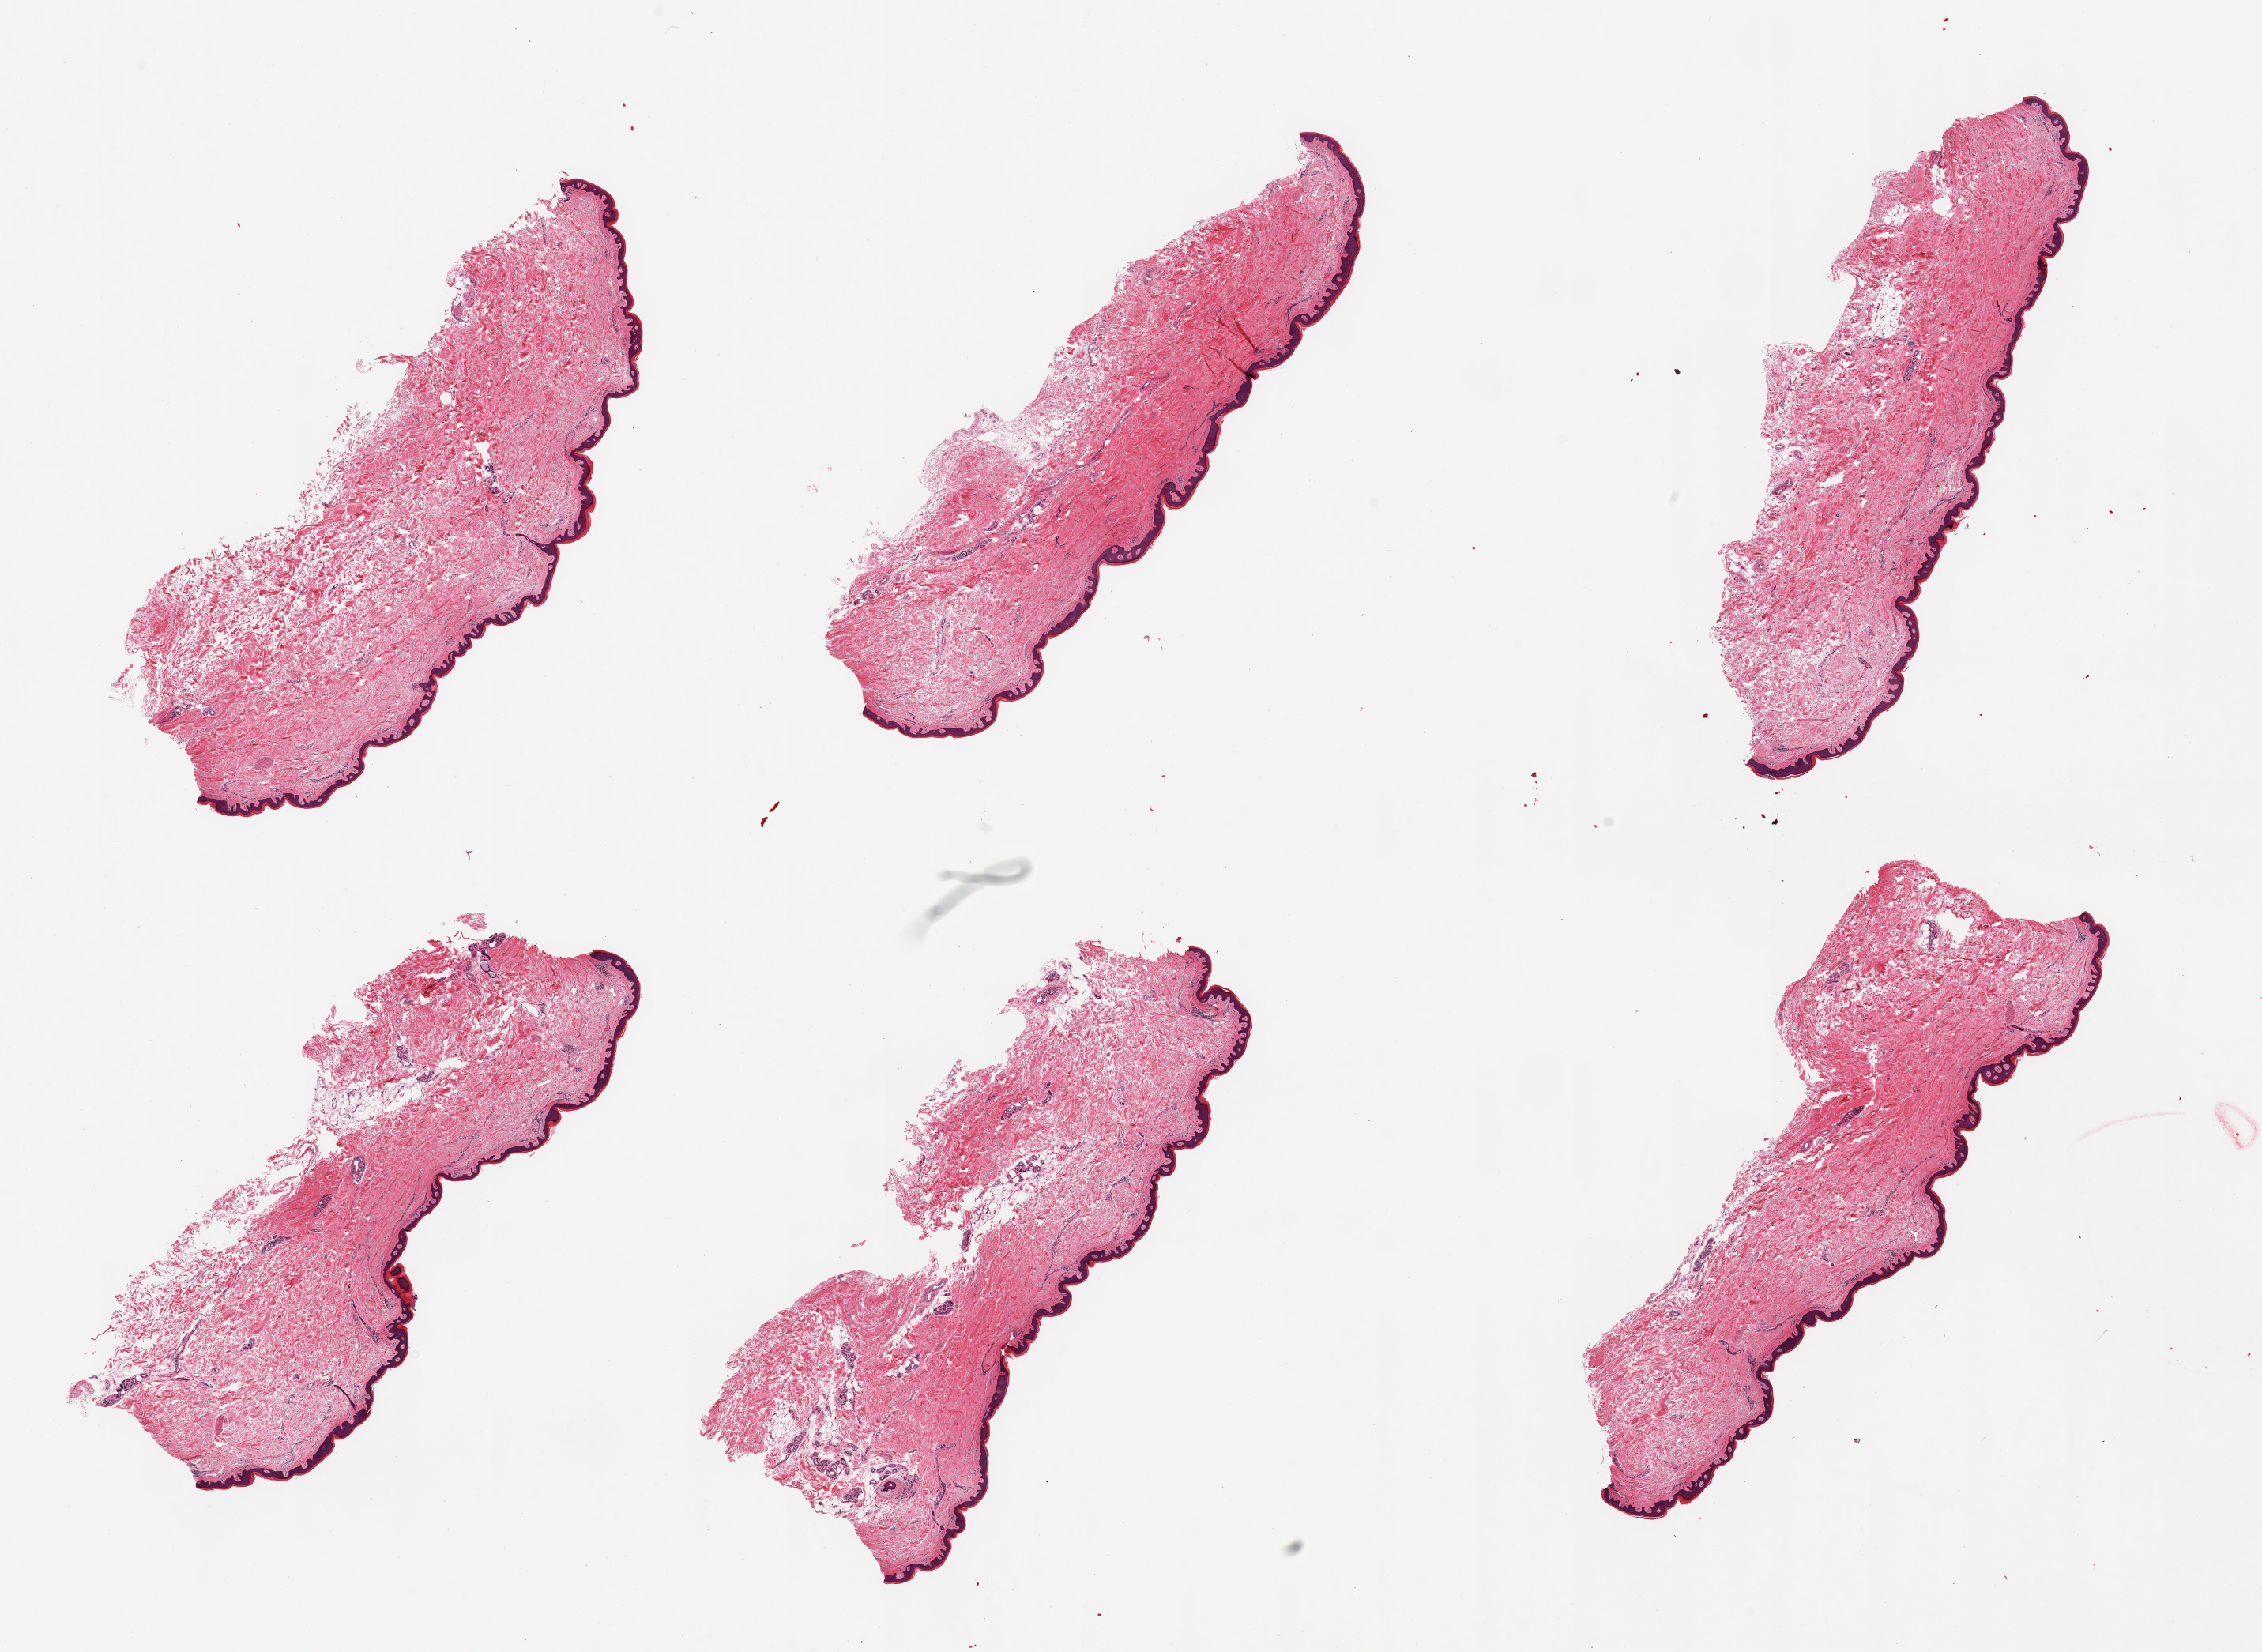
Whole-slide image, hematoxylin and eosin (H&E) stain, brightfield — whole scanned area (about 22.6 x 16.5 mm, from a 20x scan) shown as a low-resolution overview. PAXgene-fixed paraffin-embedded (PFPE) section. Section of skin of lower leg (target tissue). Donor tissue sample. Male donor.
* review note (as recorded): 6 pieces, minimal dermal fat; squamous epithelium is ~50-60 microns